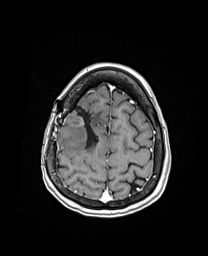
Brain MRI from a brain-tumour surgery series, one axial slice. Slice 42 of 192 in the series (ordered by position). T1-weighted post-contrast. 1 mm slice thickness. 208 × 256 image matrix. From the clinical record (not read from this slice): histopathology: Oligodendroglioma; WHO grade: 3; IDH mutation: yes; tumour location: Right Frontal.
Outlined on this slice (expert manual segmentation):
- previous resection cavity: bounding box <72,109,99,148> (left, top, right, bottom; pixels)